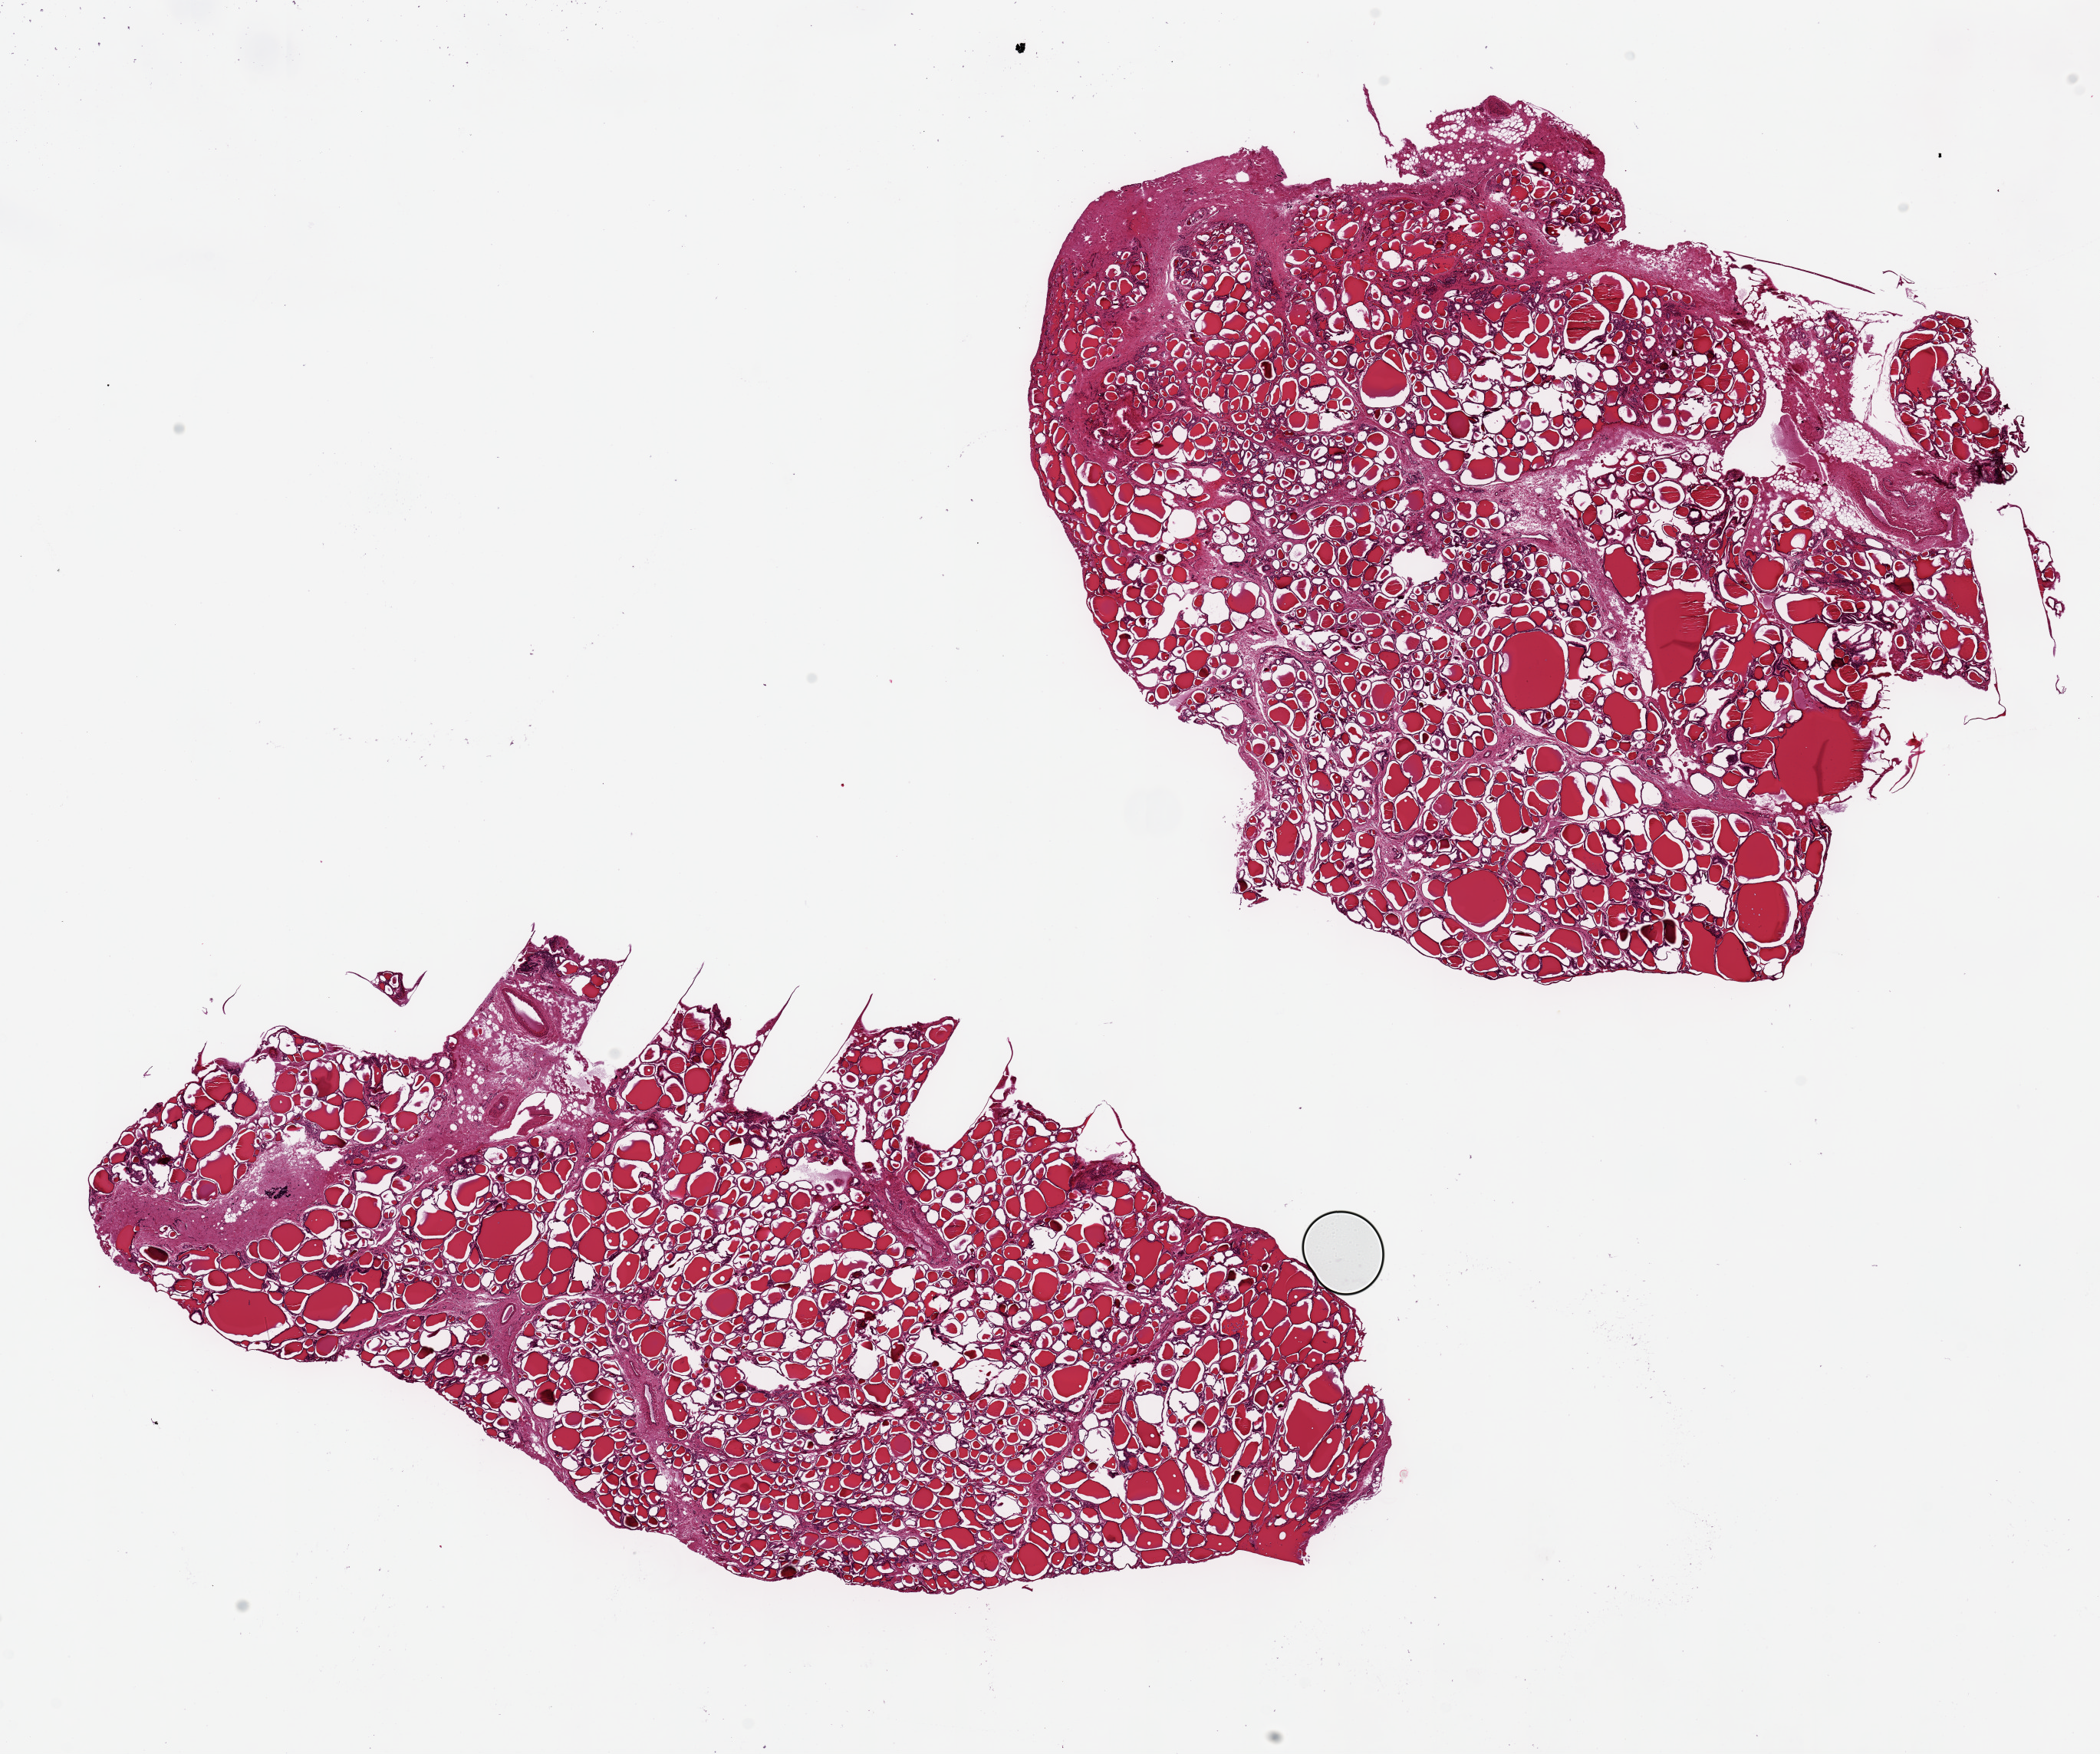
Haematoxylin and eosin whole-slide image — a low-resolution overview of the entire scanned area, about 21.7 x 18.1 mm (from a 20x scan); PAXgene-fixed, paraffin-embedded tissue; sampled site (target tissue): thyroid; donor tissue sample.
* pathologist's review note for this sample: 2 pieces ~11x8 mm